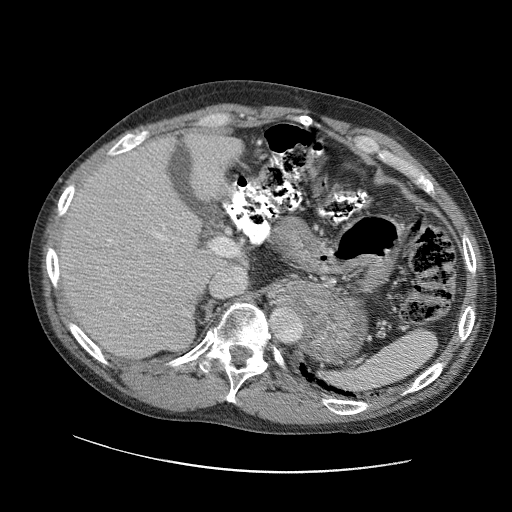
Contrast-enhanced abdominal CT (liver protocol), one axial slice; slice 69 of 109 in the series (ordered by position); reconstruction kernel STANDARD; 120 kVp; soft-tissue window (W 400 / L 40 HU); 2.5 mm slice thickness; 512 × 512 image matrix, field of view 400 × 400 mm. Case-level facts recorded for this patient, not image findings: diagnosis: hepatocellular carcinoma (patient treated with transarterial chemoembolisation; whether this scan precedes or follows treatment is not stated here); TNM stage (as recorded): Stage-IIIC; Child-Pugh class: B; tumour differentiation: well differentiated.
Annotated regions visible in this slice (semi-automatic segmentation, software-assisted and operator-edited):
- liver parenchyma outside the tumour (the mass and vessels are separate outlines, so this box may not span the whole liver): bounding box (x1, y1, x2, y2) in pixels: (56, 130, 242, 358)
- mass: (157, 315, 195, 350)
- liver vessels: (108, 169, 220, 323)